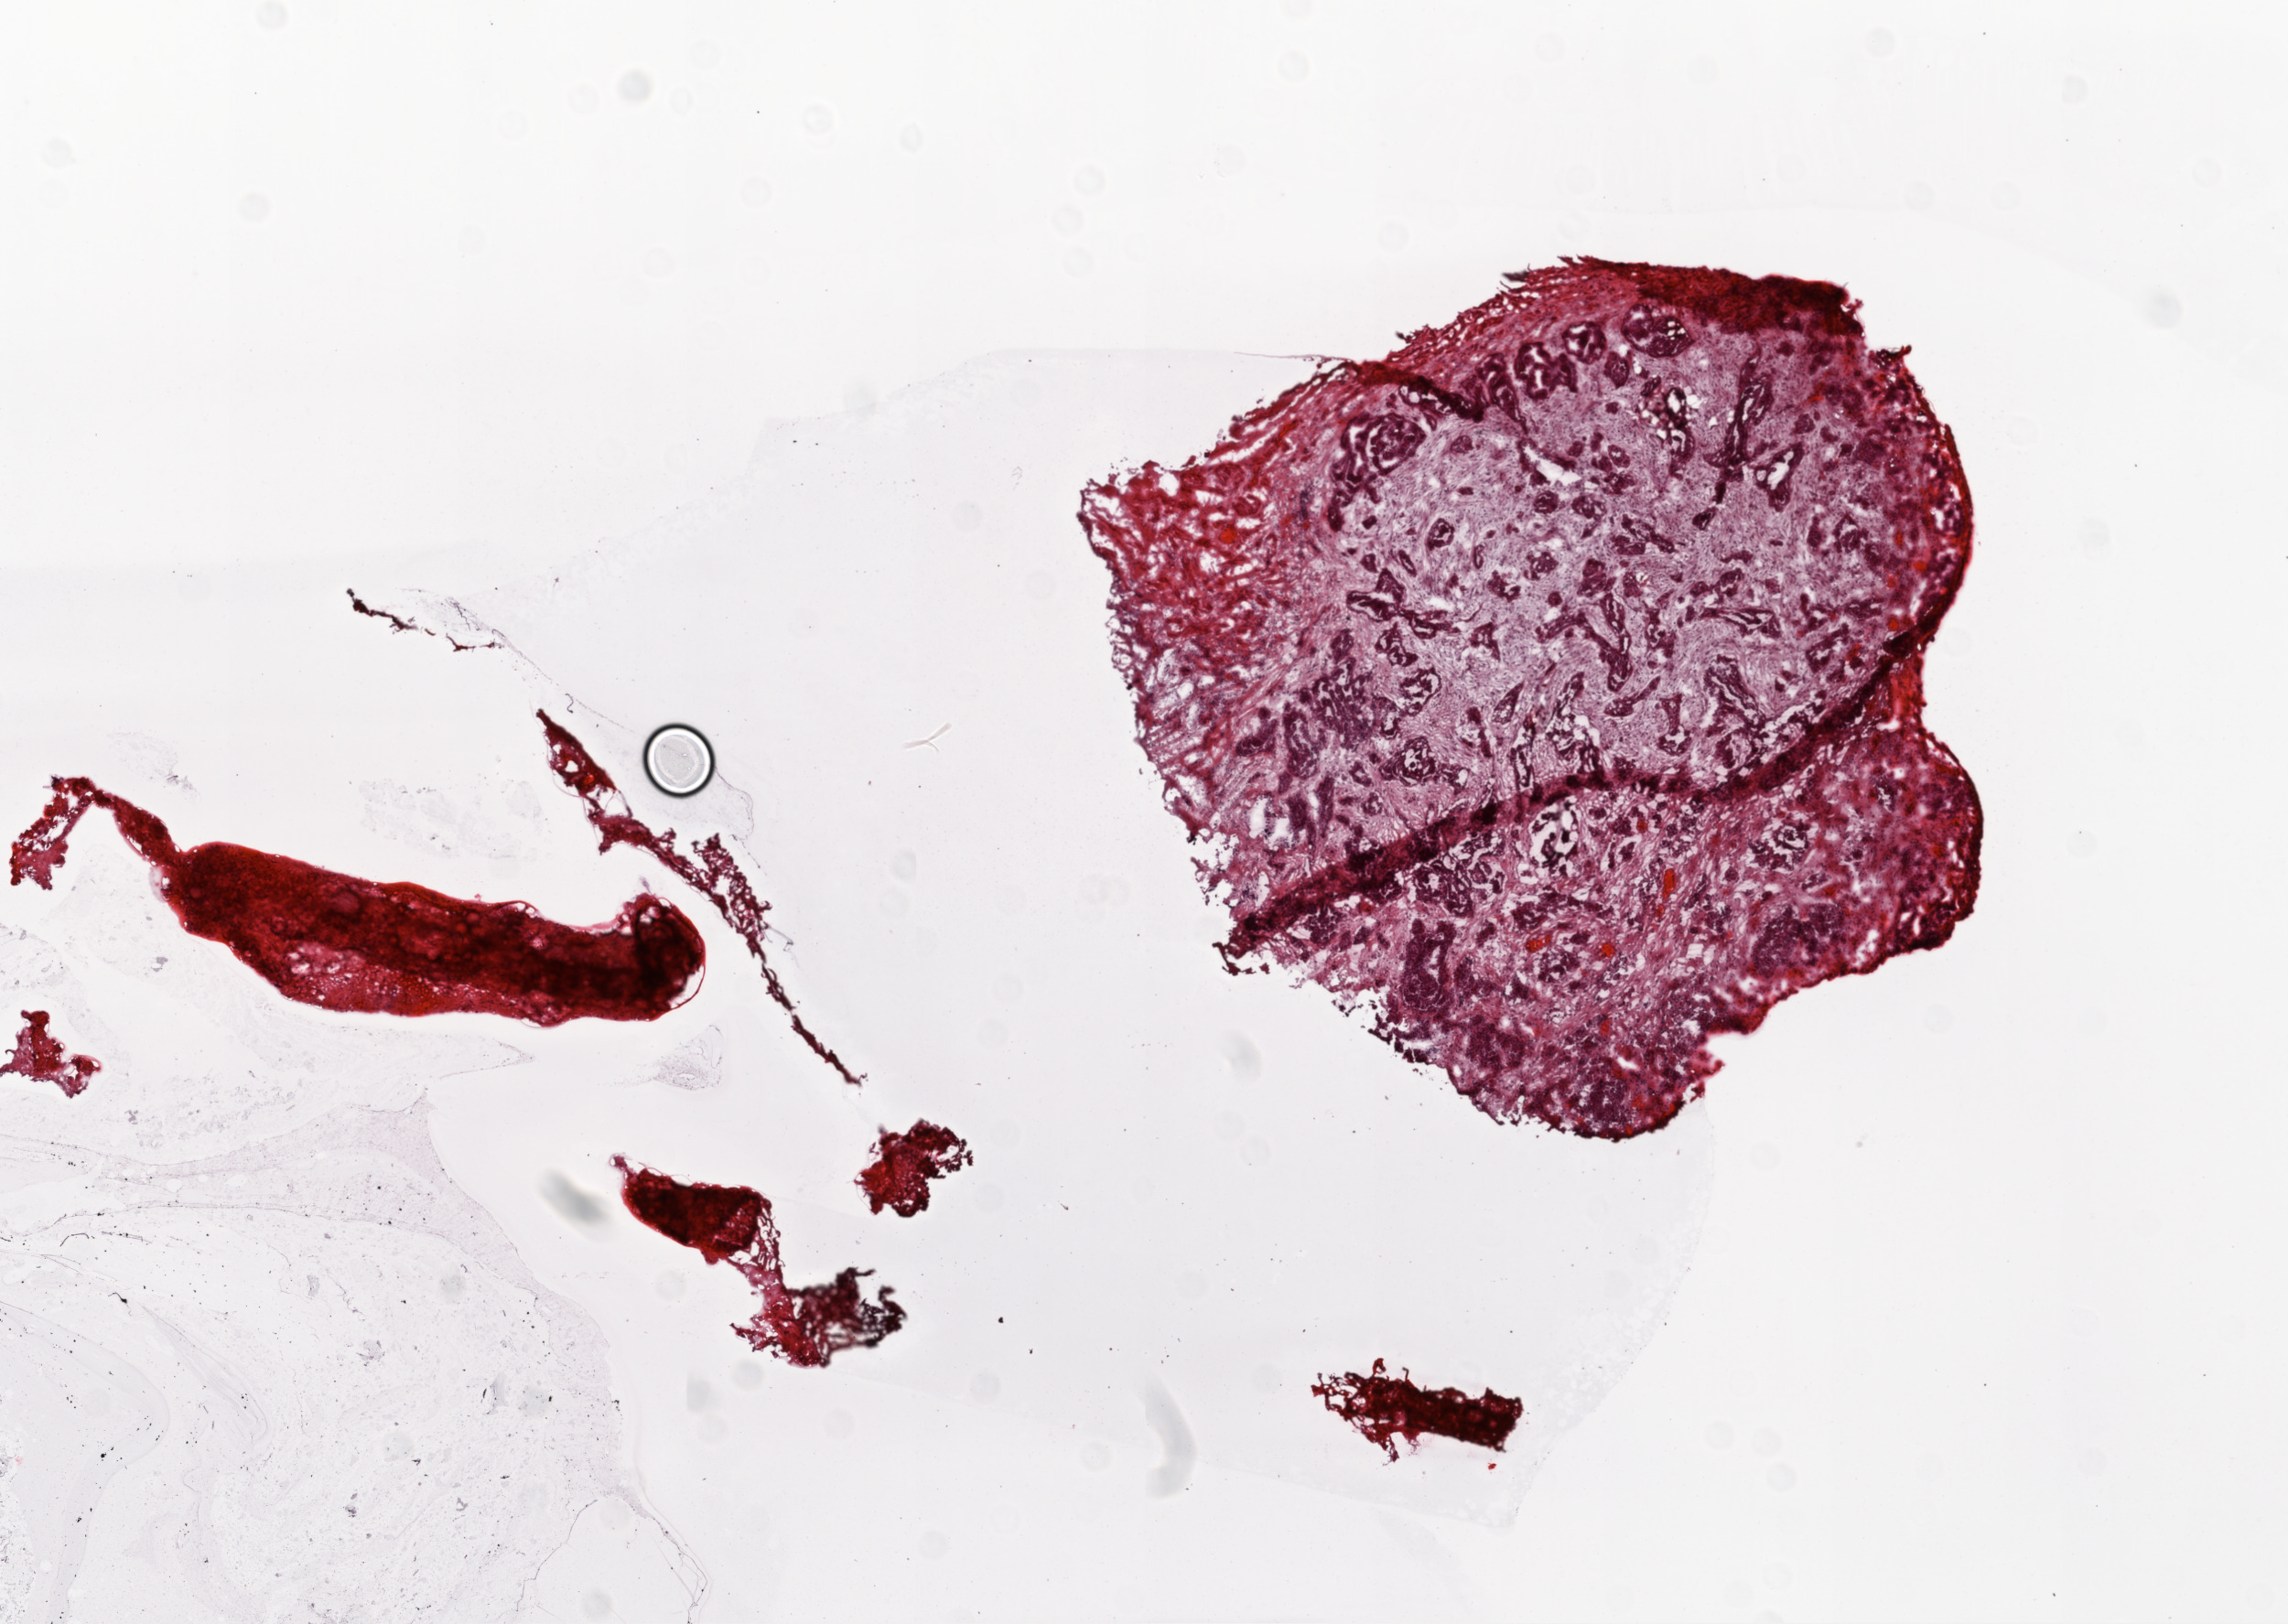
Whole-slide histology image, Hematoxylin and eosin (H&E) stained, shown as a low-resolution overview of the whole scanned area (about 10.0 x 7.1 mm, acquisition: 20x scan), frozen section from the top of the tissue portion, sample: primary tumour, ovary. Patient: female, age at initial diagnosis 65 years. Histologic grade: G3 (poorly differentiated). Slide review estimates, as recorded: tumour cells 50%, tumour nuclei 90%, normal cells 0%, stromal cells 50%, necrosis 0%. Infiltration values recorded for this section: lymphocyte infiltration 0%, monocyte infiltration 0%, neutrophil infiltration 0%.
FIGO stage: IIIC. Pathologic diagnosis: Serous cystadenocarcinoma, NOS.